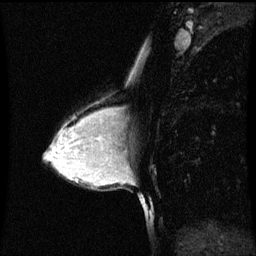
Breast MRI (dynamic contrast-enhanced), one sagittal slice. Slice 39 of 60 in the series (ordered by position). Dynamic contrast-enhanced series, image 2 of 3 at this slice position (ordered by acquisition). 1.5 T. TE 4.2 ms, TR 8.9 ms. 2 mm slice thickness. 256 × 256 image matrix. Female patient, age 33 years. From the clinical record (not read from this slice): setting: breast cancer imaged before/during neoadjuvant chemotherapy; receptor status: HER2-positive.
Structures marked on this image (semi-automatic segmentation, software-assisted and operator-edited):
- analysis volume of interest (the breast-tissue region the enhancement analysis was run in; not a lesion): bounding box (x1, y1, x2, y2) in pixels: (107, 108, 121, 147)
- tumour enhancement mask (voxels above the 70 % enhancement threshold inside the analysis volume of interest): (107, 108, 115, 137)